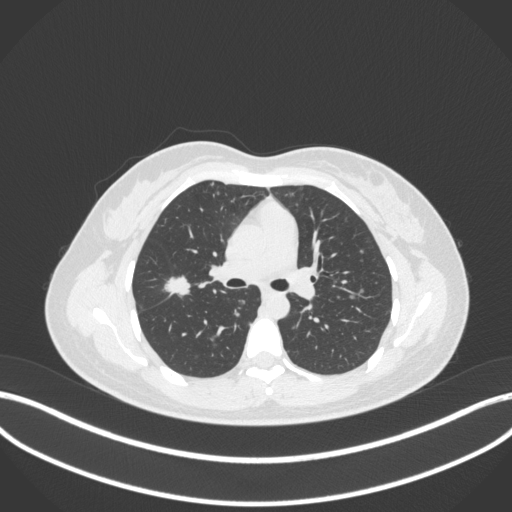
Chest CT, one axial slice. Slice 204 of 214 in the series (ordered by position). Lung window (W 1500 / L -600 HU). 1 mm slice thickness. 512 × 512 image matrix, field of view 400 × 400 mm. Patient: female, 33 years. From the clinical record (not read from this slice): clinical TNM (as recorded): T1c N0 M0.
Structures marked on this image (bounding box drawn by a radiologist):
- lung tumour (recorded histology: adenocarcinoma): bounding box <162,269,196,300> (left, top, right, bottom; pixels)